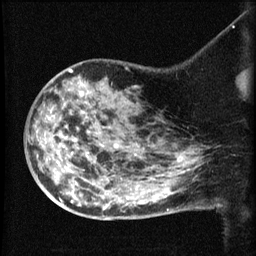
Breast MRI (dynamic contrast-enhanced), one sagittal slice. Slice 41 of 60 in the series (ordered by position). Dynamic contrast-enhanced series, image 2 of 3 at this slice position (ordered by acquisition). 1.5 T. TE 4.2 ms, TR 8.2 ms. 2.1 mm slice thickness. 256 × 256 image matrix, field of view 180 × 180 mm. Patient: female, 50 years.
Outlined on this slice (semi-automatic segmentation, software-assisted and operator-edited):
- analysis volume of interest (the breast-tissue region the enhancement analysis was run in; not a lesion): bounding box <38,75,169,211> (left, top, right, bottom; pixels)
- tumour enhancement mask (voxels above the 70 % enhancement threshold inside the analysis volume of interest): <81,92,83,94>